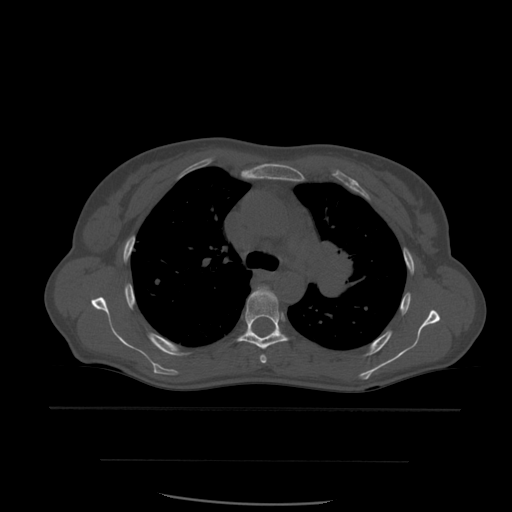
CT including the spine, one axial slice; position 412 of 574 along the scan axis; bone window (W 1800 / L 400 HU); 512 × 512 image matrix, field of view 392 × 392 mm. Patient age 48 years. Case-level facts recorded for this patient, not image findings: primary cancer: lung.
Outlined on this slice (semi-automatic segmentation, software-assisted and operator-edited):
- T4 vertebra: bounding box [x1, y1, x2, y2] px = [260, 354, 267, 364]
- T5 vertebra: [237, 287, 289, 350]